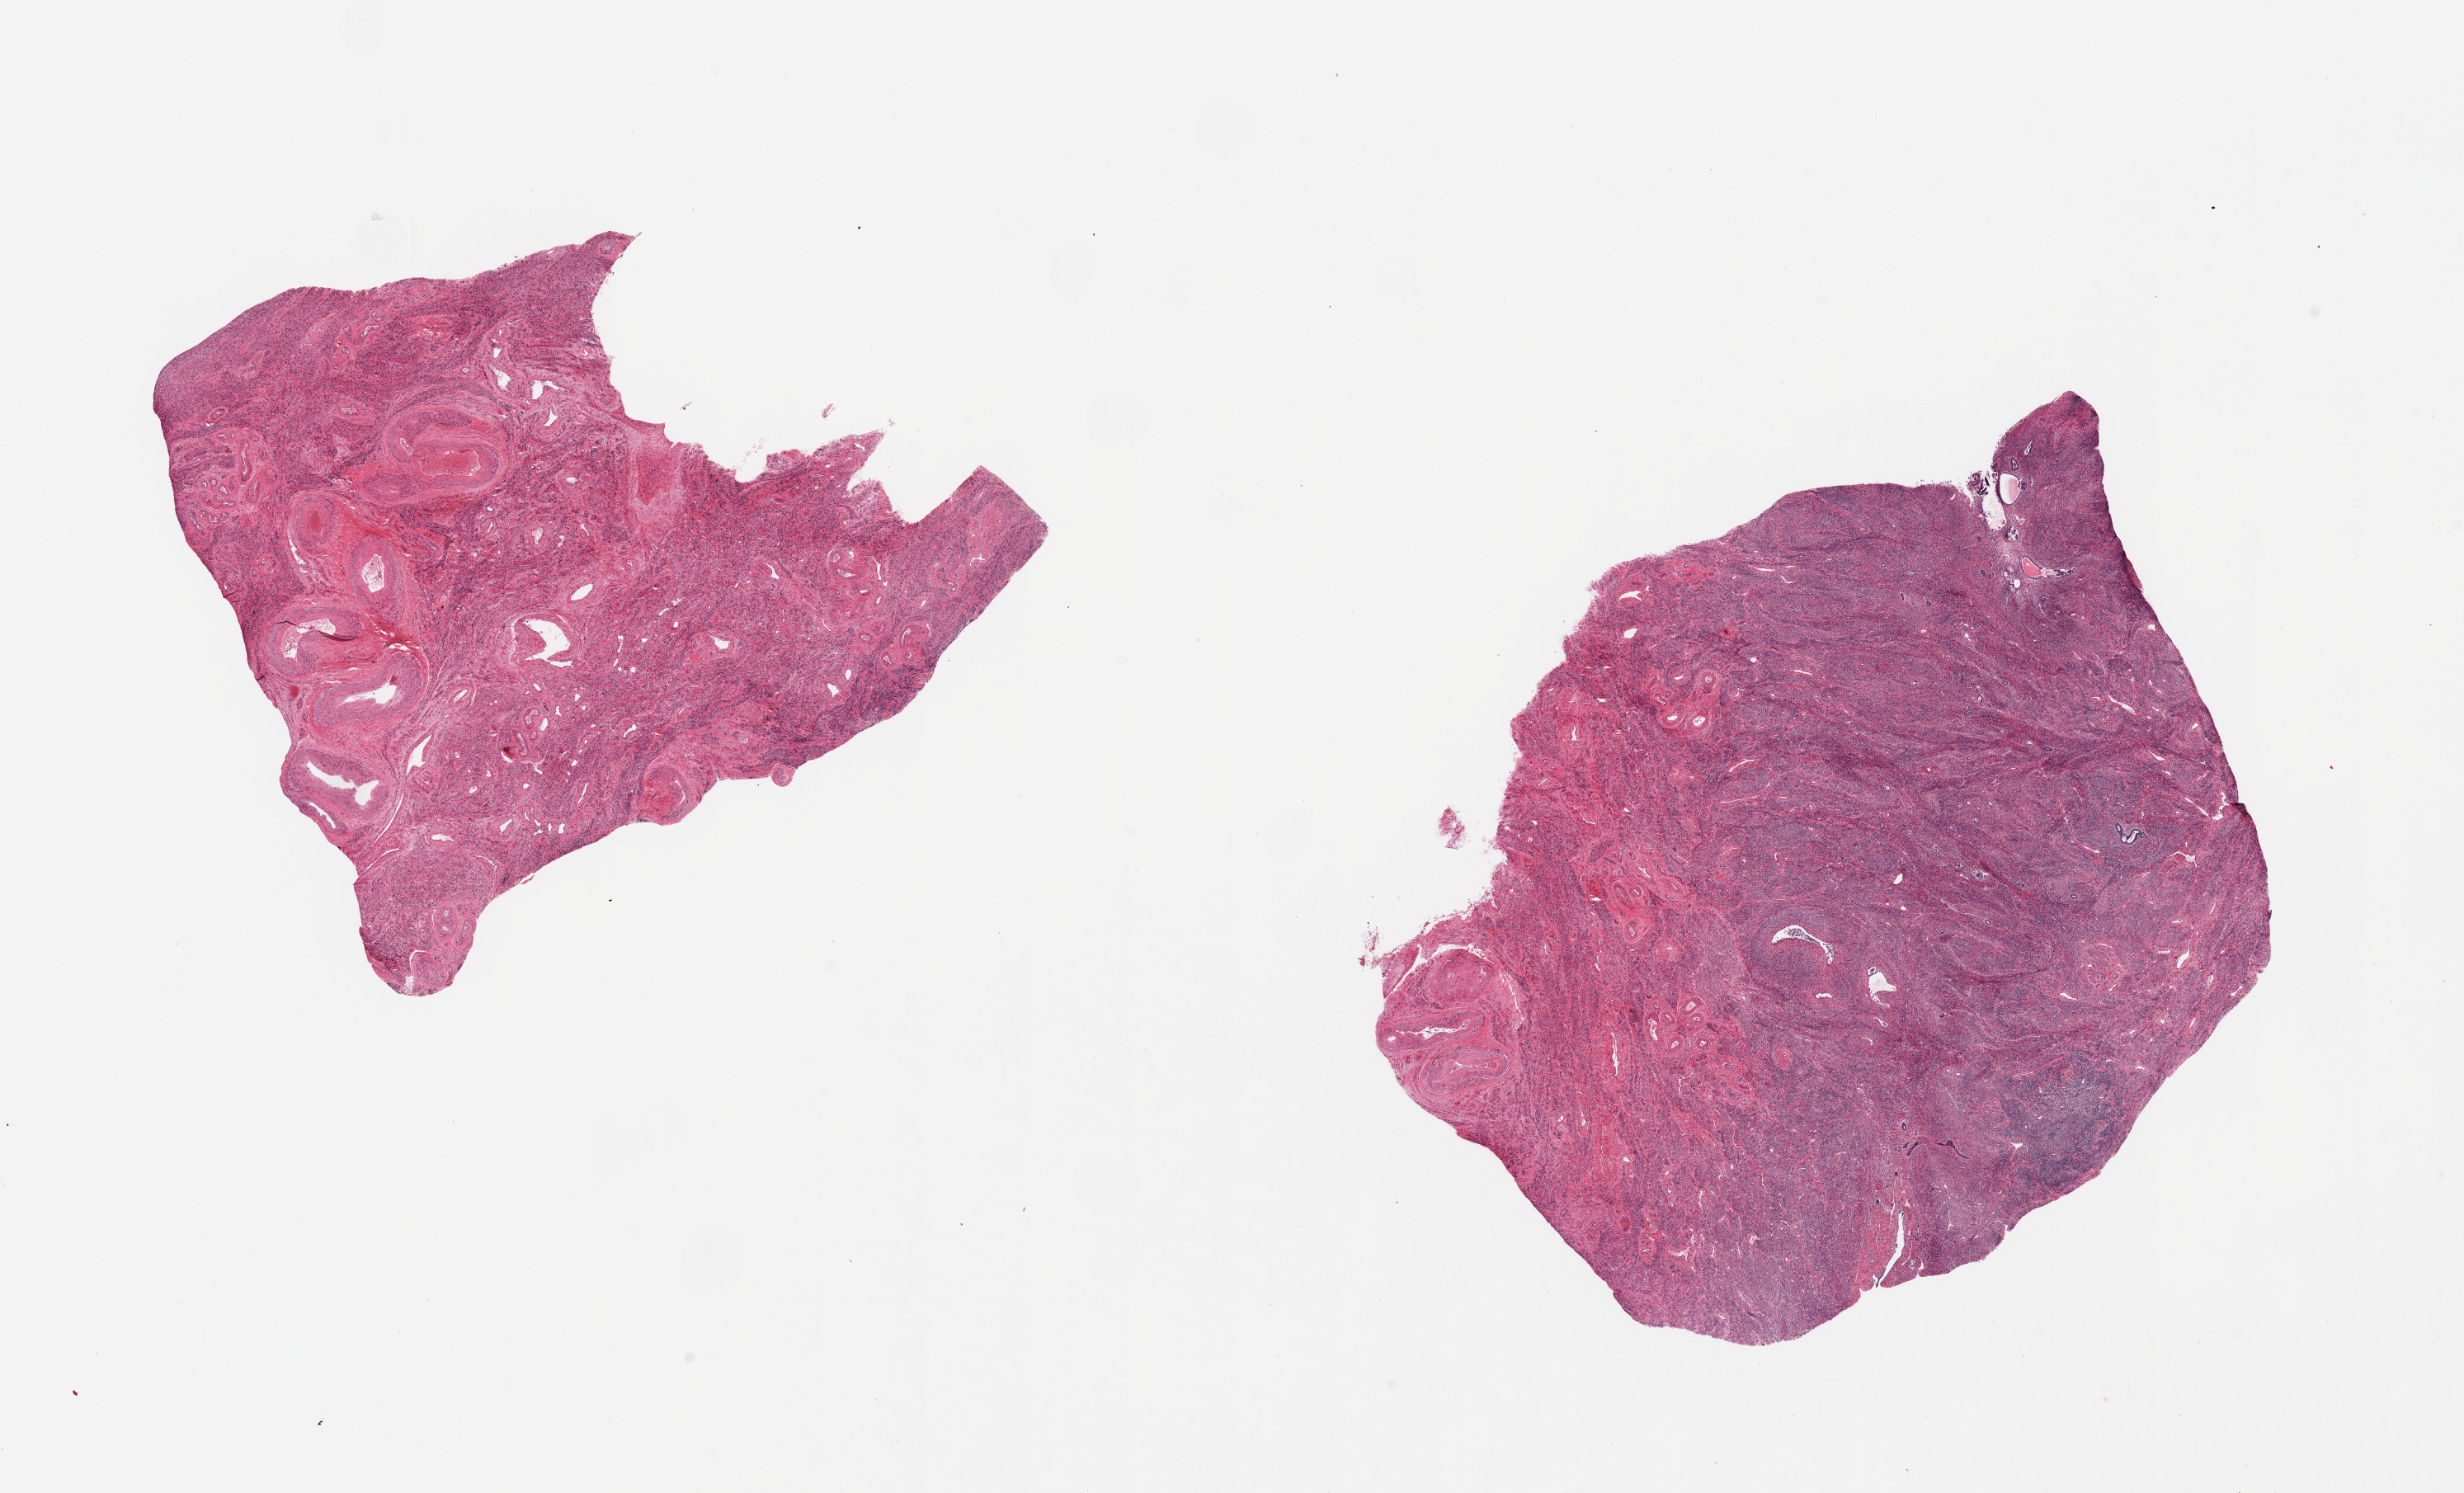
Whole-slide image, H&E stain — low-resolution overview of the scanned area, about 23.6 x 14.3 mm (from a 20x scan), PAXgene-fixed, paraffin-embedded tissue, target tissue: uterus, donor tissue sample. Donor: female.
Reviewer comment on this tissue sample: 2 pieces; atrophic endometrium and adenomyosis.